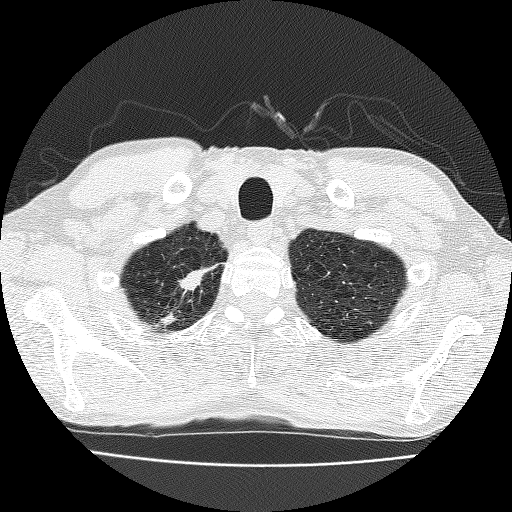
Low-dose screening chest CT, axial slice. Third screening round (two years after baseline). Lung window (W 1500 / L -600 HU). 2 mm slice thickness. 120 kVp. Slice 26 of 185 in the series. 512 × 512 image matrix. Male participant, aged 63 years at enrolment. Current smoker at enrolment.
- Expert reader's lesion annotation, bounding box [x1, y1, x2, y2] px = [146, 257, 226, 329].
- Reader record for this screening exam (exam-level; its link to the box is not recorded): non-calcified nodule or mass ≥4 mm, right upper lobe, 17 × 10 mm, spiculated (stellate) margins, soft tissue attenuation, pre-existing on the prior screen: yes; interval growth: yes.
- Official screen result: positive, other.
- Lung cancer was diagnosed 28 days after this screen: adenocarcinoma, NOS, right upper lobe, moderately differentiated (G2), stage IIIB (AJCC 6th edition), 17 mm at pathology.